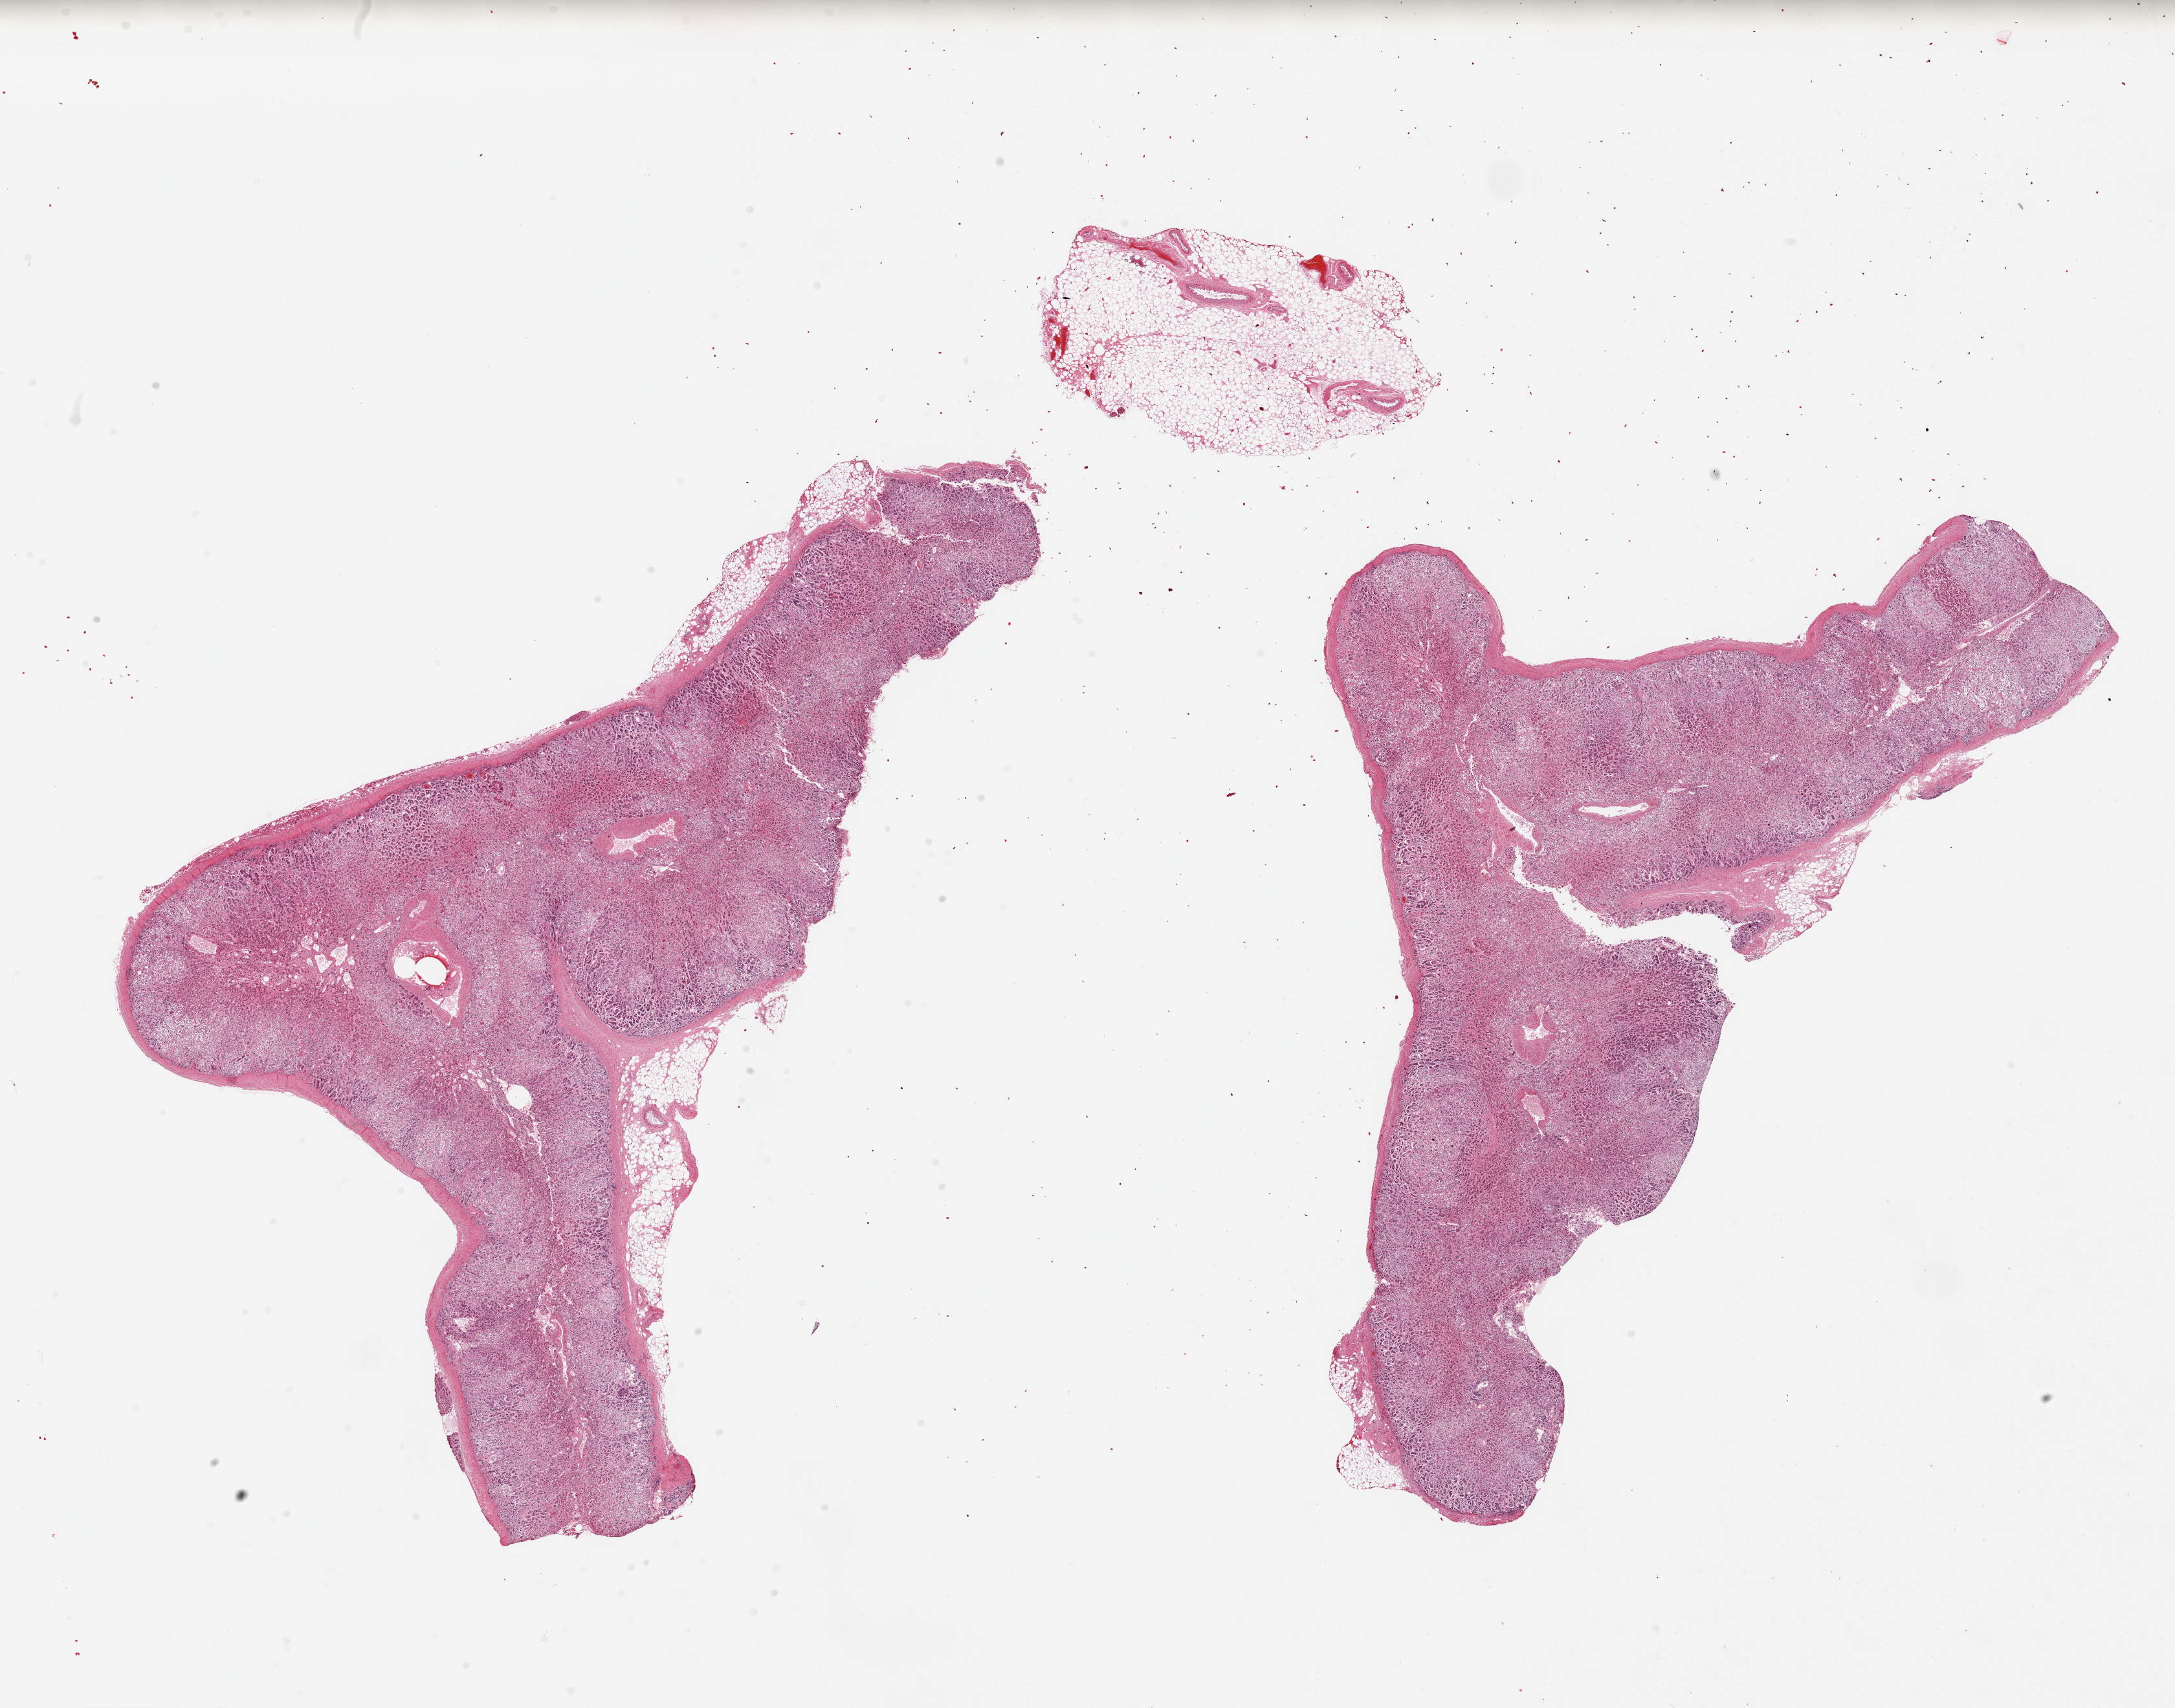
Haematoxylin and eosin whole-slide image, low-resolution overview of the scanned area, about 26.6 x 20.9 mm, PAXgene-fixed, paraffin-embedded tissue, section of adrenal gland (target tissue), donor tissue sample. Donor sex: male.
• review note (as recorded): 2 pieces; moderately autolyzed, small attachment and detached fragment of fat